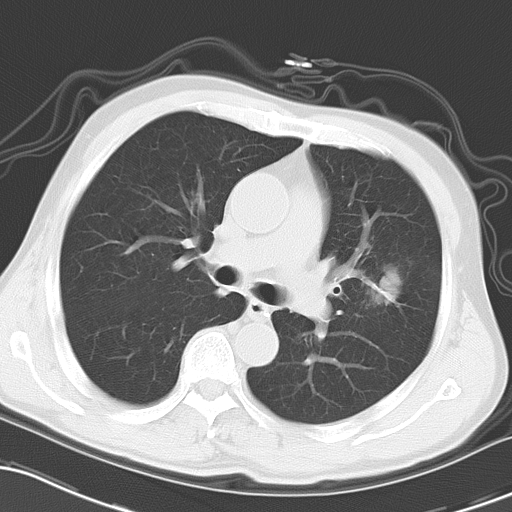
Chest CT, one axial slice. Slice 16 of 27 in the series (ordered by position). Reconstruction kernel B70f. 120 kVp. Lung window (W 1500 / L -600 HU). 10 mm slice thickness. 512 × 512 image matrix, field of view 318 × 318 mm. Male patient, age 60 years. From the clinical record (not read from this slice): clinical TNM (as recorded): T1c N1 M0.
Outlined on this slice (bounding box drawn by a radiologist):
- lung tumour (recorded histology: adenocarcinoma): box from (x=365, y=261) to (x=407, y=314) px
- lung tumour (recorded histology: adenocarcinoma): (x=372, y=259)–(x=410, y=309)